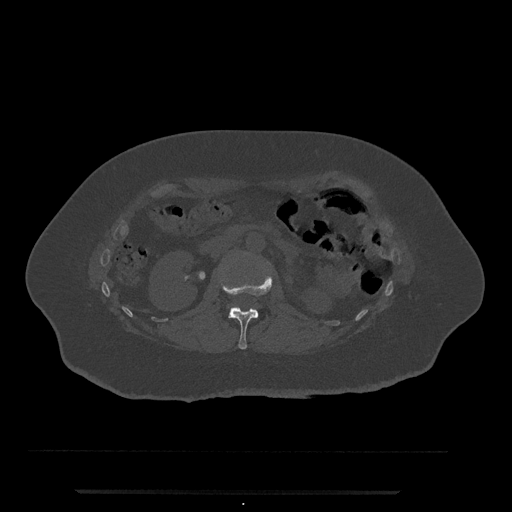
CT including the spine, one axial slice; slice 83 of 797 in the series (ordered by position); reconstruction kernel Br40s/3; 120 kVp; bone window (W 1800 / L 400 HU); 0.5 mm slice thickness; 512 × 512 image matrix, field of view 440 × 440 mm. Female patient, age 51 years. Case-level facts recorded for this patient, not image findings: primary cancer: neuro; vertebrae with lytic lesions (as recorded): T8.
Outlined on this slice (semi-automatic segmentation, software-assisted and operator-edited):
- L1 vertebra: bounding box (x1, y1, x2, y2) in pixels: (220, 275, 273, 350)
- L2 vertebra: (229, 306, 238, 311)